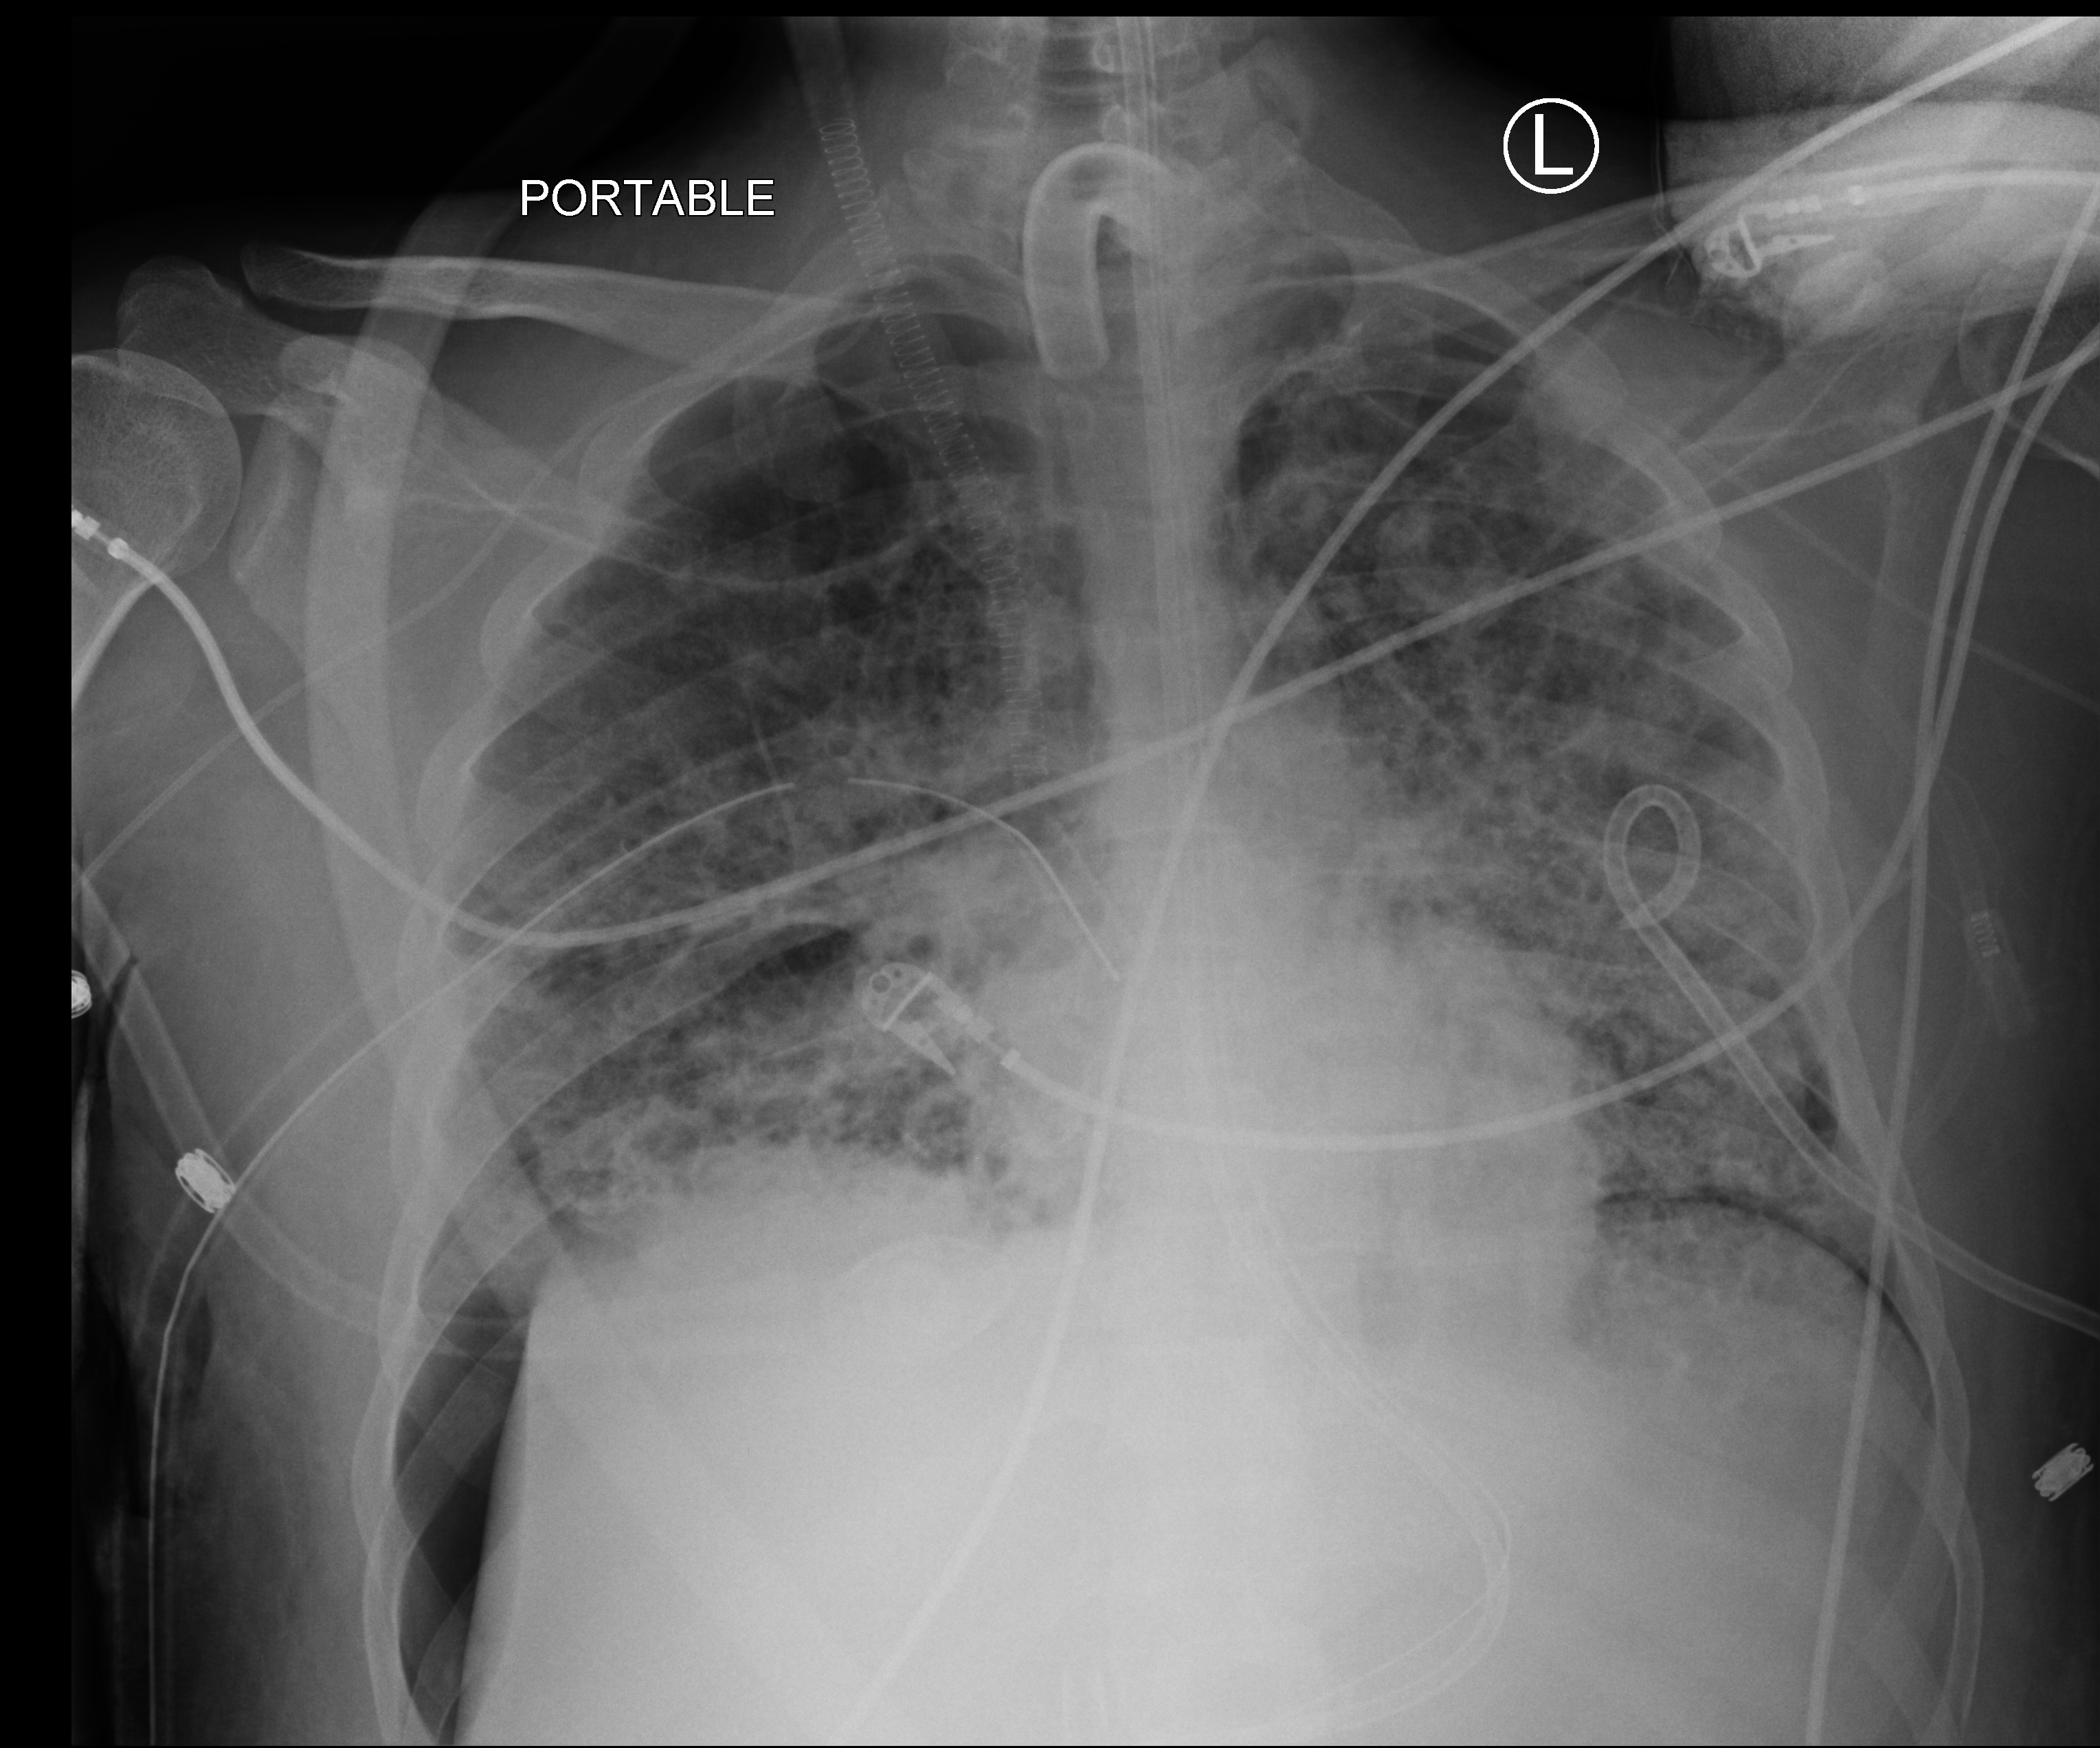
Portable chest radiograph; anteroposterior (AP) projection. Patient hospitalised with COVID-19, aged 18–59 years.
Admission-level facts for this patient (not findings on this image; timing relative to this image not recorded):
- length of hospital stay: 60 days
- COPD (admission record): no
- admitted to intensive care during this hospital stay: yes